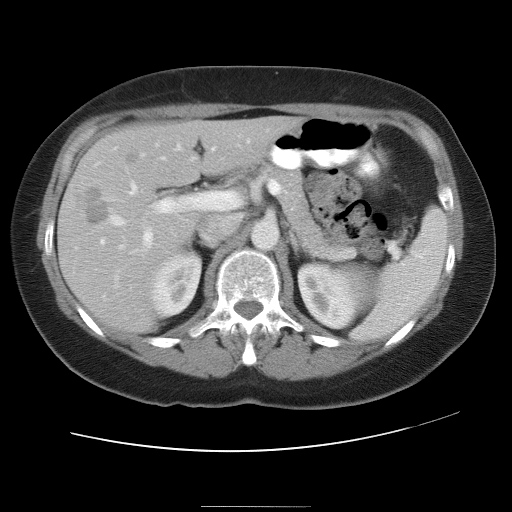
Contrast-enhanced abdominal CT, one axial slice; slice 19 of 30 in the series (ordered by position); reconstruction kernel STANDARD; soft-tissue window (W 400 / L 40 HU); 7.5 mm slice thickness; 512 × 512 image matrix, field of view 376 × 376 mm. Female patient, age 52 years. Case-level facts recorded for this patient, not image findings: diagnosis: colorectal cancer liver metastases, imaged before liver resection; multiple liver metastases: no; largest metastasis: 3 cm; disease in both lobes: yes.
Structures marked on this image (manually delineated by an expert):
- hepatic veins: bounding box (x1, y1, x2, y2) in pixels: (110, 157, 164, 226)
- liver: (58, 117, 293, 332)
- planned liver remnant (the part of the liver to remain after resection): (143, 117, 293, 184)
- portal vein (with intrahepatic branches): (100, 146, 214, 246)
- liver metastasis: (129, 155, 138, 162)
- liver metastasis: (86, 188, 110, 221)